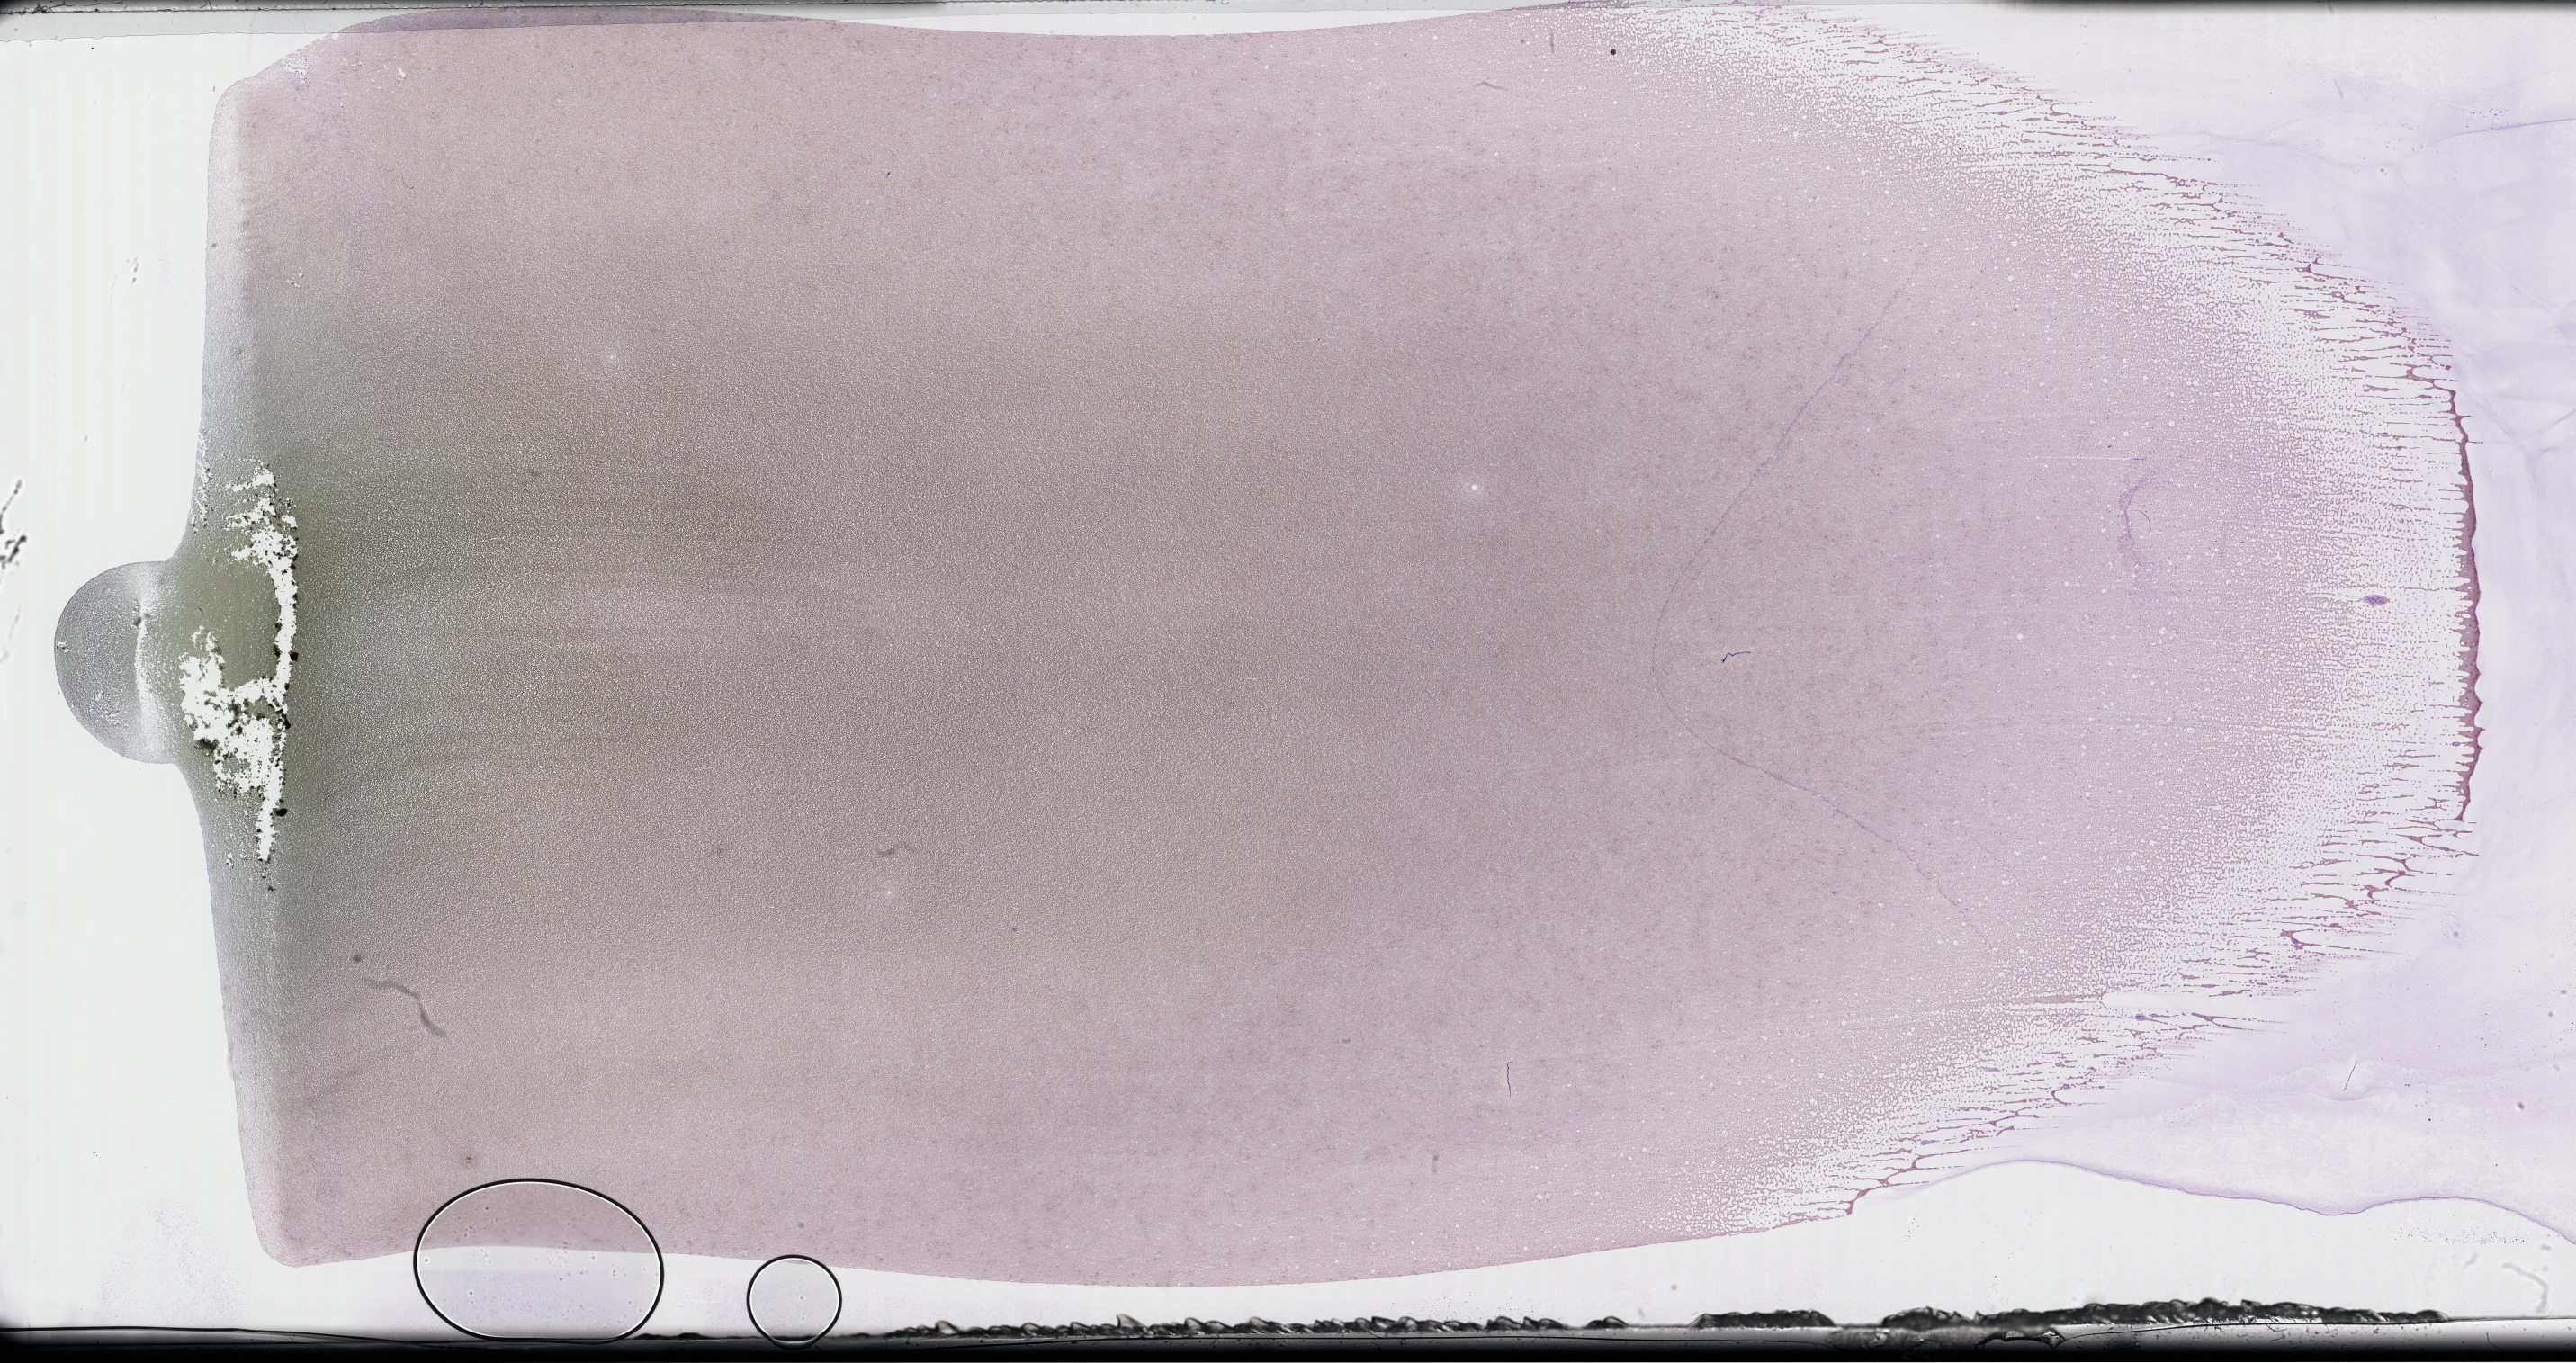
Whole-slide image of a whole blood smear, Wright-Giemsa stain, a low-resolution overview of the entire scanned area, about 46.2 x 24.5 mm, specimen time point: collected on treatment. Male patient.
- patient diagnosis: Plasma Cell Myeloma